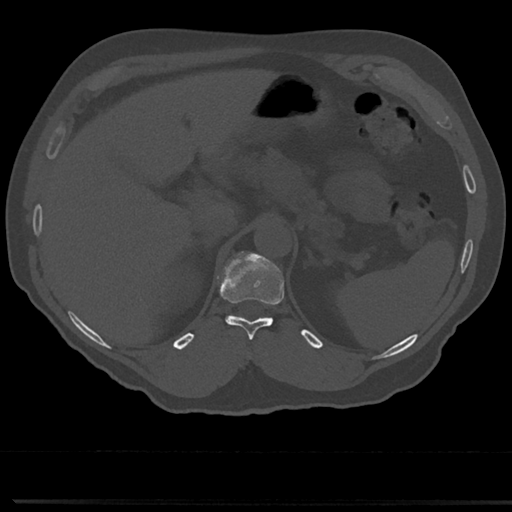
CT including the spine, one axial slice; position 192 of 817 along the scan axis; reconstruction kernel Br40s/3; 120 kVp; bone window (W 1800 / L 400 HU); 0.5 mm slice thickness; 512 × 512 image matrix, field of view 355 × 355 mm. Patient: male, 61 years. Case-level facts recorded for this patient, not image findings: primary cancer: prostate.
Annotated regions visible in this slice (semi-automatically segmented with operator editing):
- T11 vertebra: bounding box <223,258,284,342> (left, top, right, bottom; pixels)
- T12 vertebra: <244,255,255,258>